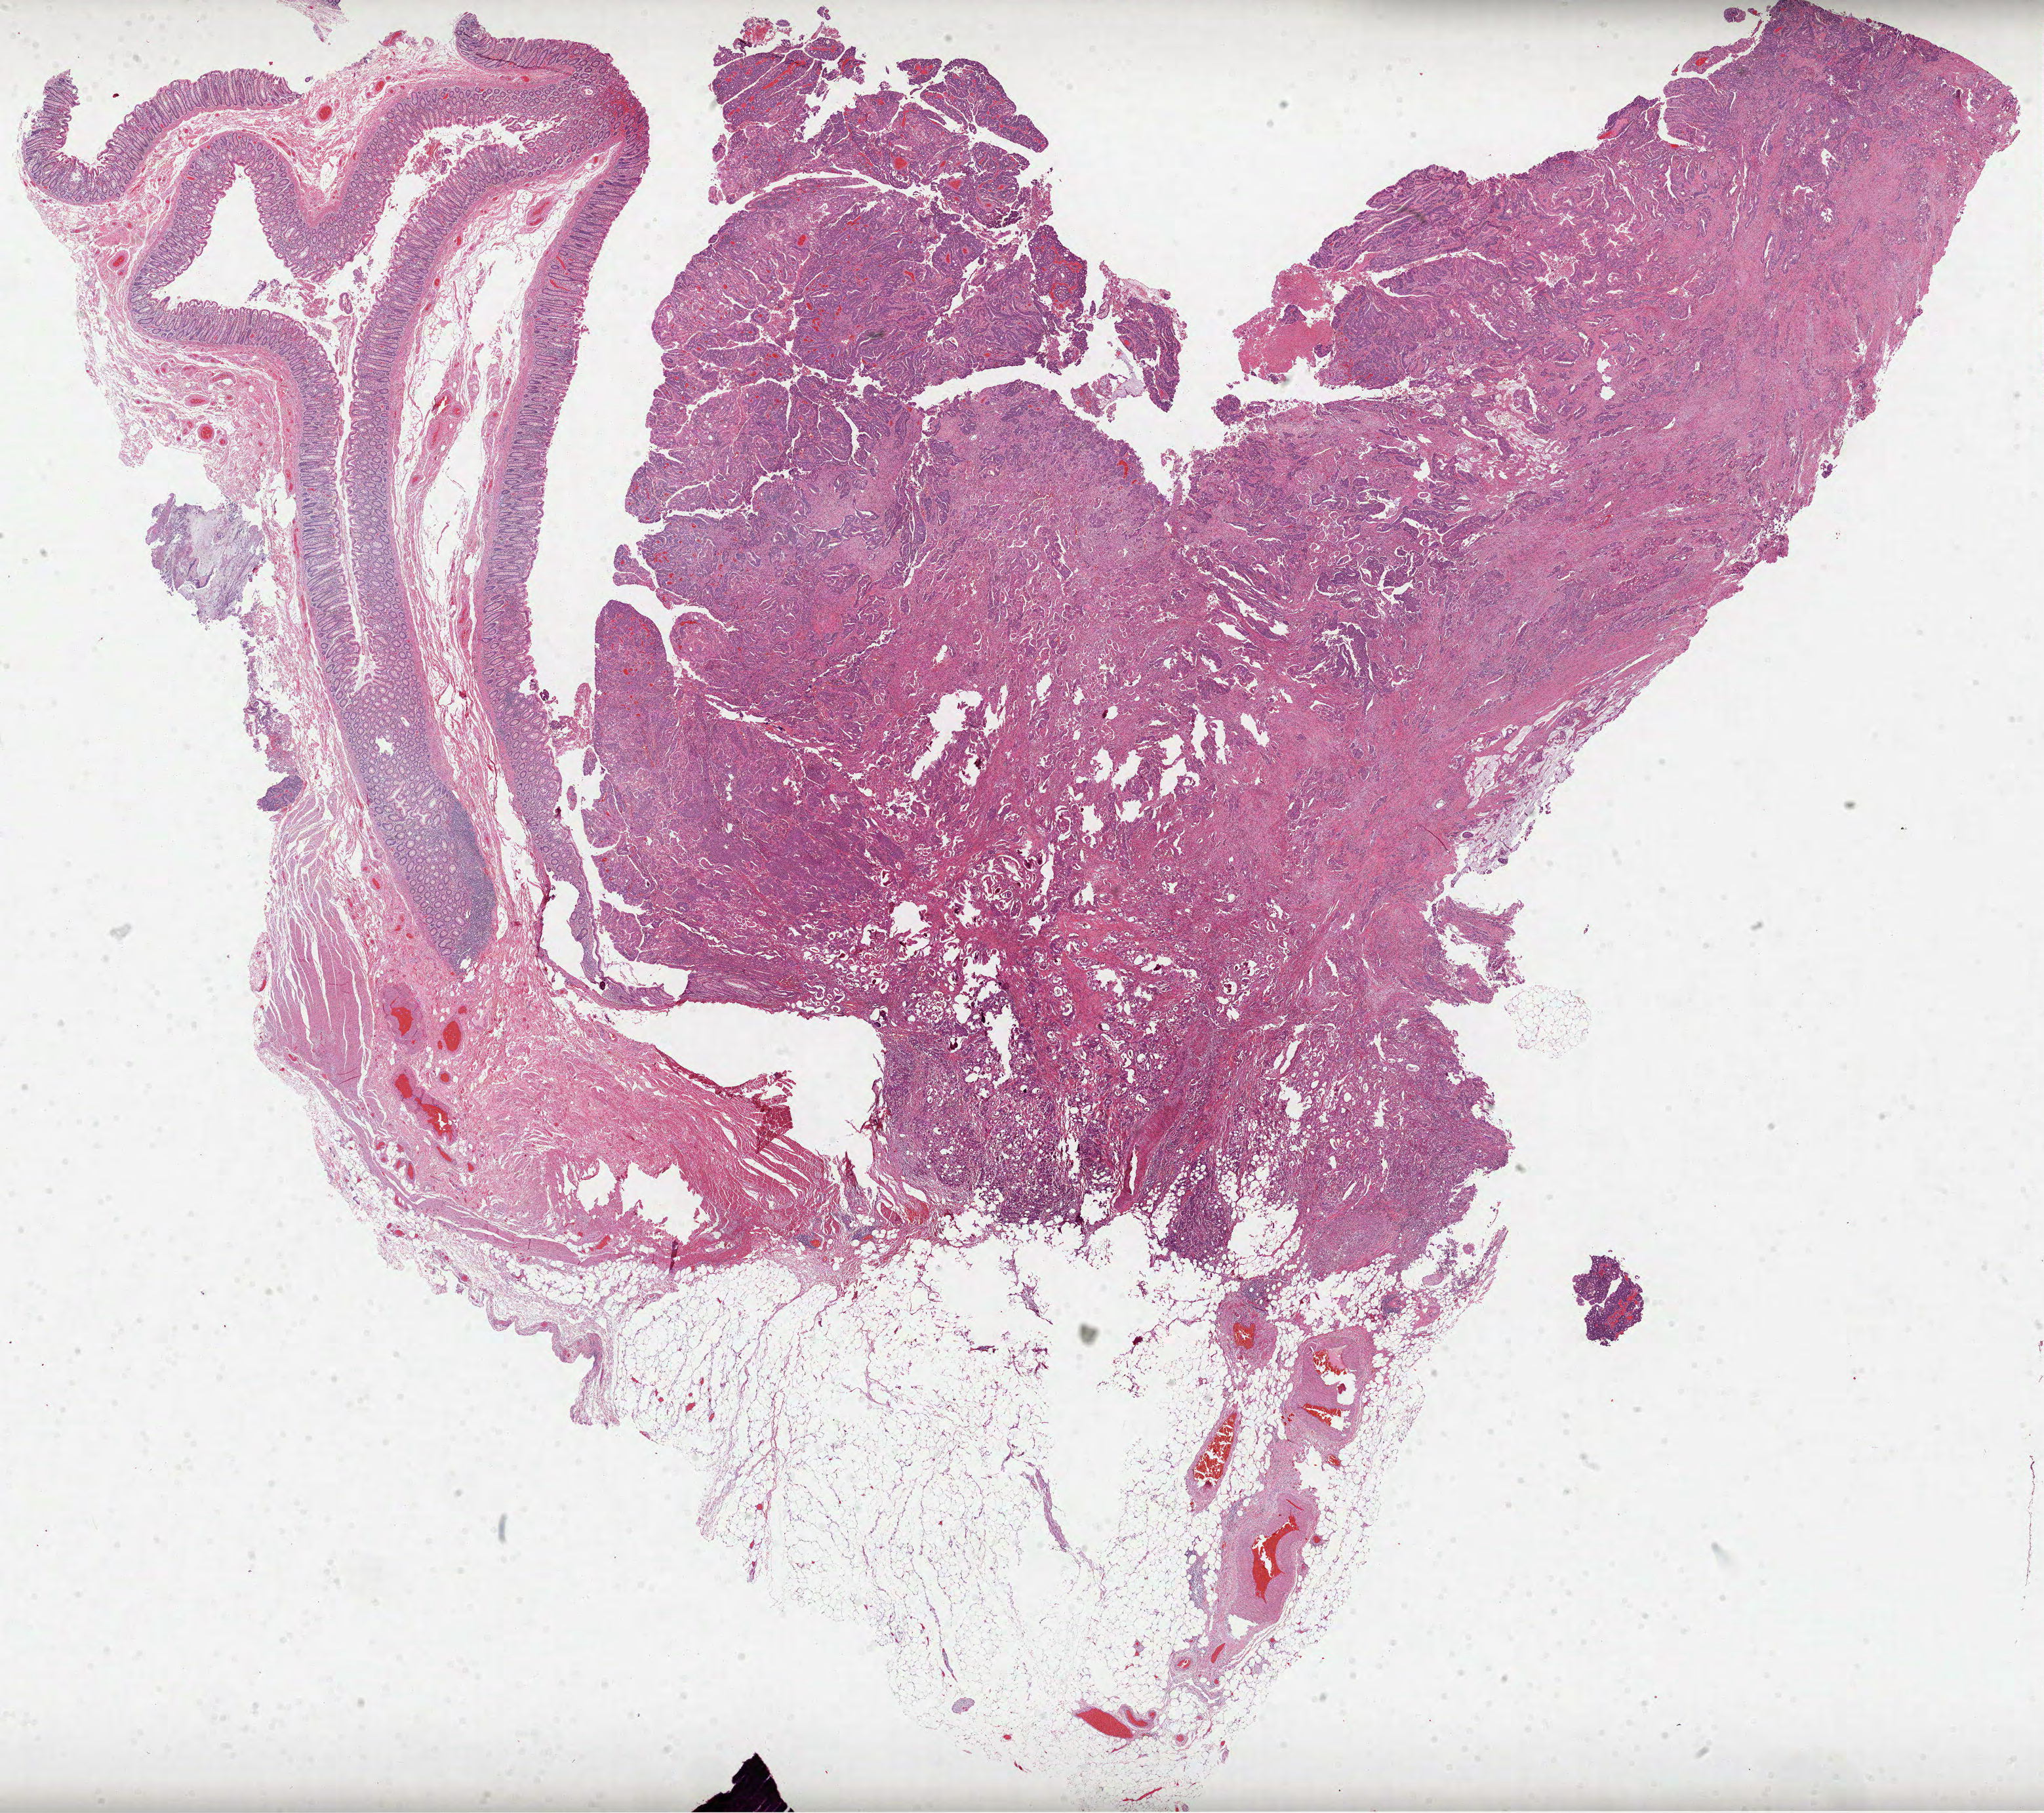
Digitized H&E tissue section (whole slide) — whole scanned area (about 25.1 x 22.3 mm, acquisition: 40x scan) shown as a low-resolution overview. Formalin-fixed paraffin-embedded (FFPE) diagnostic section. Colon, primary tumour sample. Male, age 84 years at initial diagnosis.
Histologic diagnosis: Adenocarcinoma, NOS. AJCC pathologic stage: IIIB. TNM: T3 N1 M0.